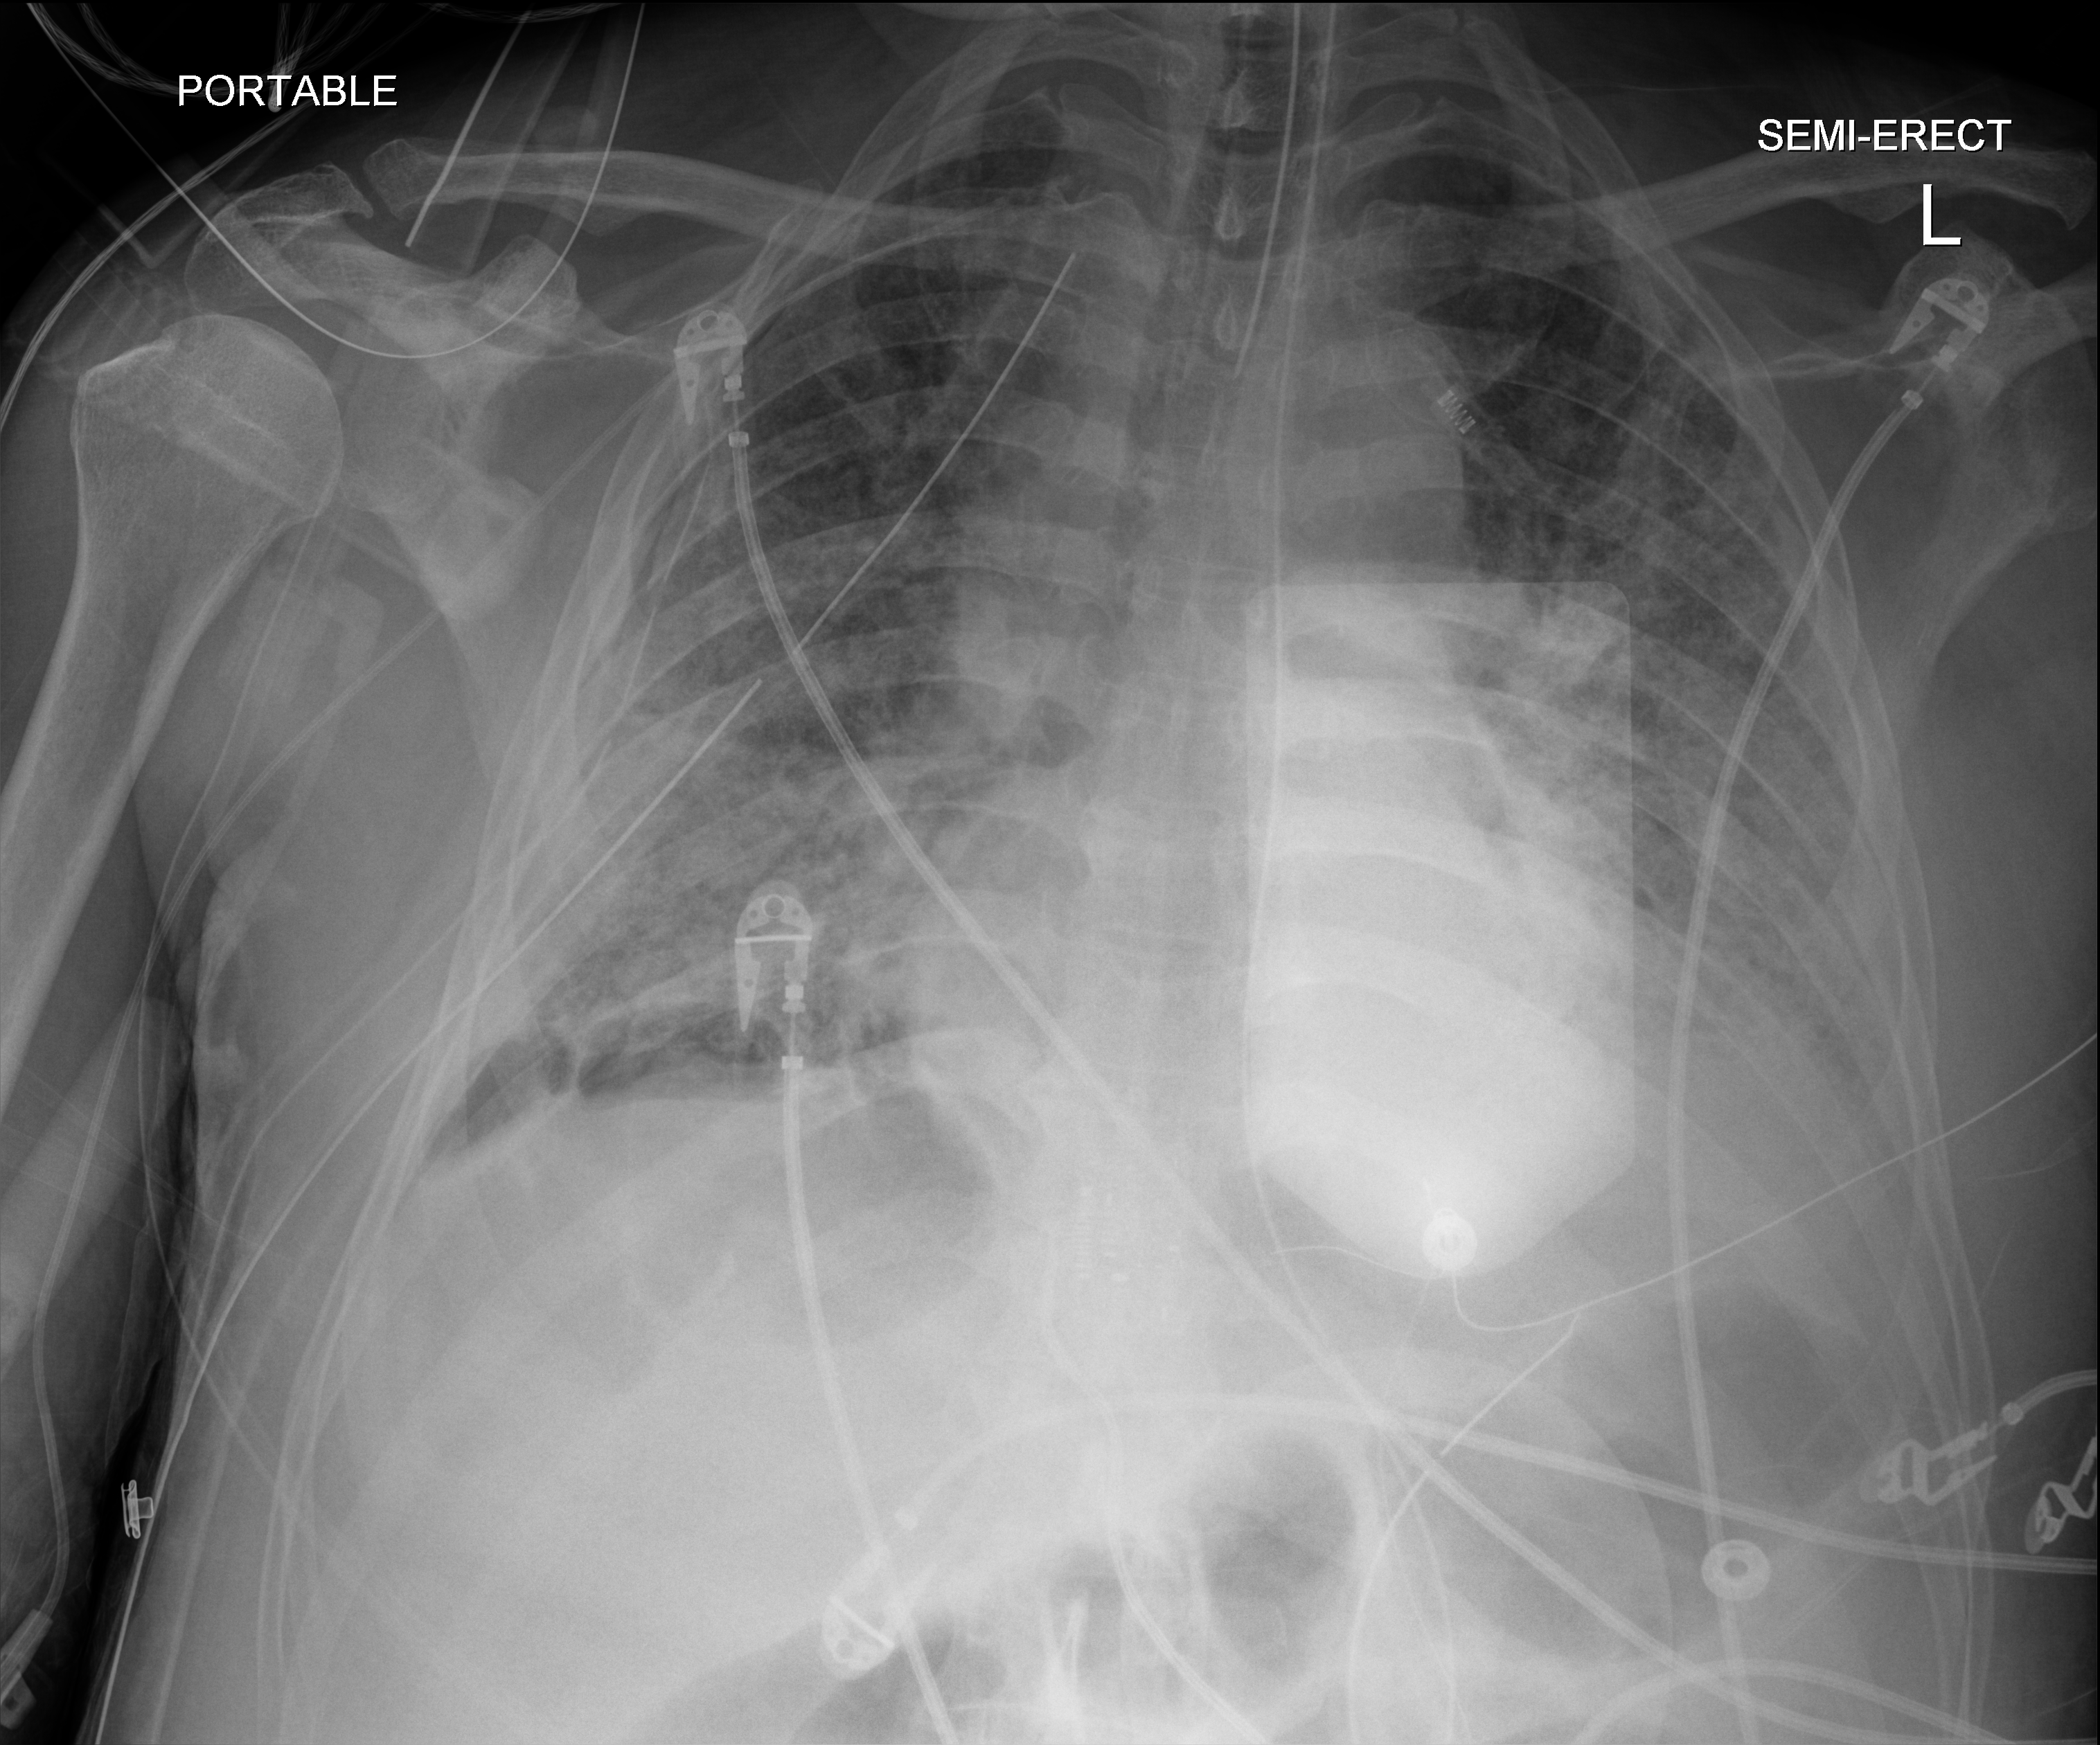
Chest X-ray, anteroposterior (AP) projection. Patient hospitalised with COVID-19; male, aged 60–74 years.
Hospital-stay facts (about this admission, not read from this image; timing relative to this image not recorded): mechanically ventilated during this hospital stay: yes.